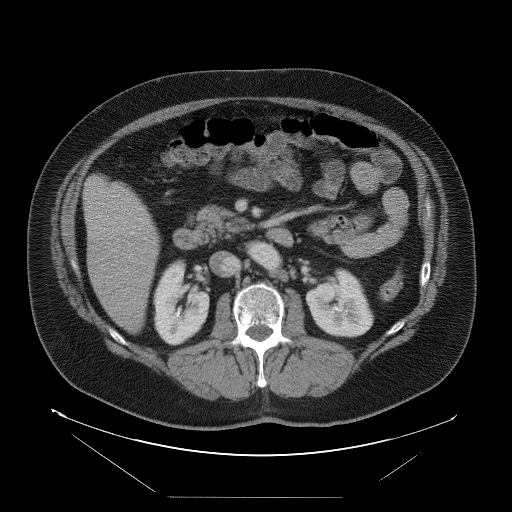
Contrast-enhanced abdominal CT, one axial slice; slice 34 of 114 in the series (ordered by position); intravenous contrast given; soft-tissue window (W 400 / L 40 HU); 5 mm slice thickness; 512 × 512 image matrix. Male patient, age 61 years. From the clinical record (not read from this slice): diagnosis: colorectal cancer liver metastases, imaged before liver resection; multiple liver metastases: no; largest metastasis: 6.5 cm; disease in both lobes: yes.
Annotated regions visible in this slice (expert manual segmentation):
- liver: bounding box (x1, y1, x2, y2) in pixels: (84, 177, 160, 333)